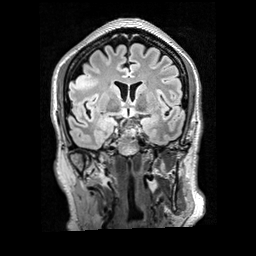
Brain MRI from a brain-tumour surgery series, one coronal slice. Position 115 of 200 along the scan axis. T2 FLAIR. 1 mm slice thickness. 256 × 256 image matrix, field of view 256 × 256 mm. Case-level facts recorded for this patient, not image findings: histopathology: Glioblastoma; WHO grade: 4; IDH mutation: no.
Outlined on this slice (expert manual segmentation):
- tumour: bounding box (x1, y1, x2, y2) in pixels: (71, 71, 99, 91)